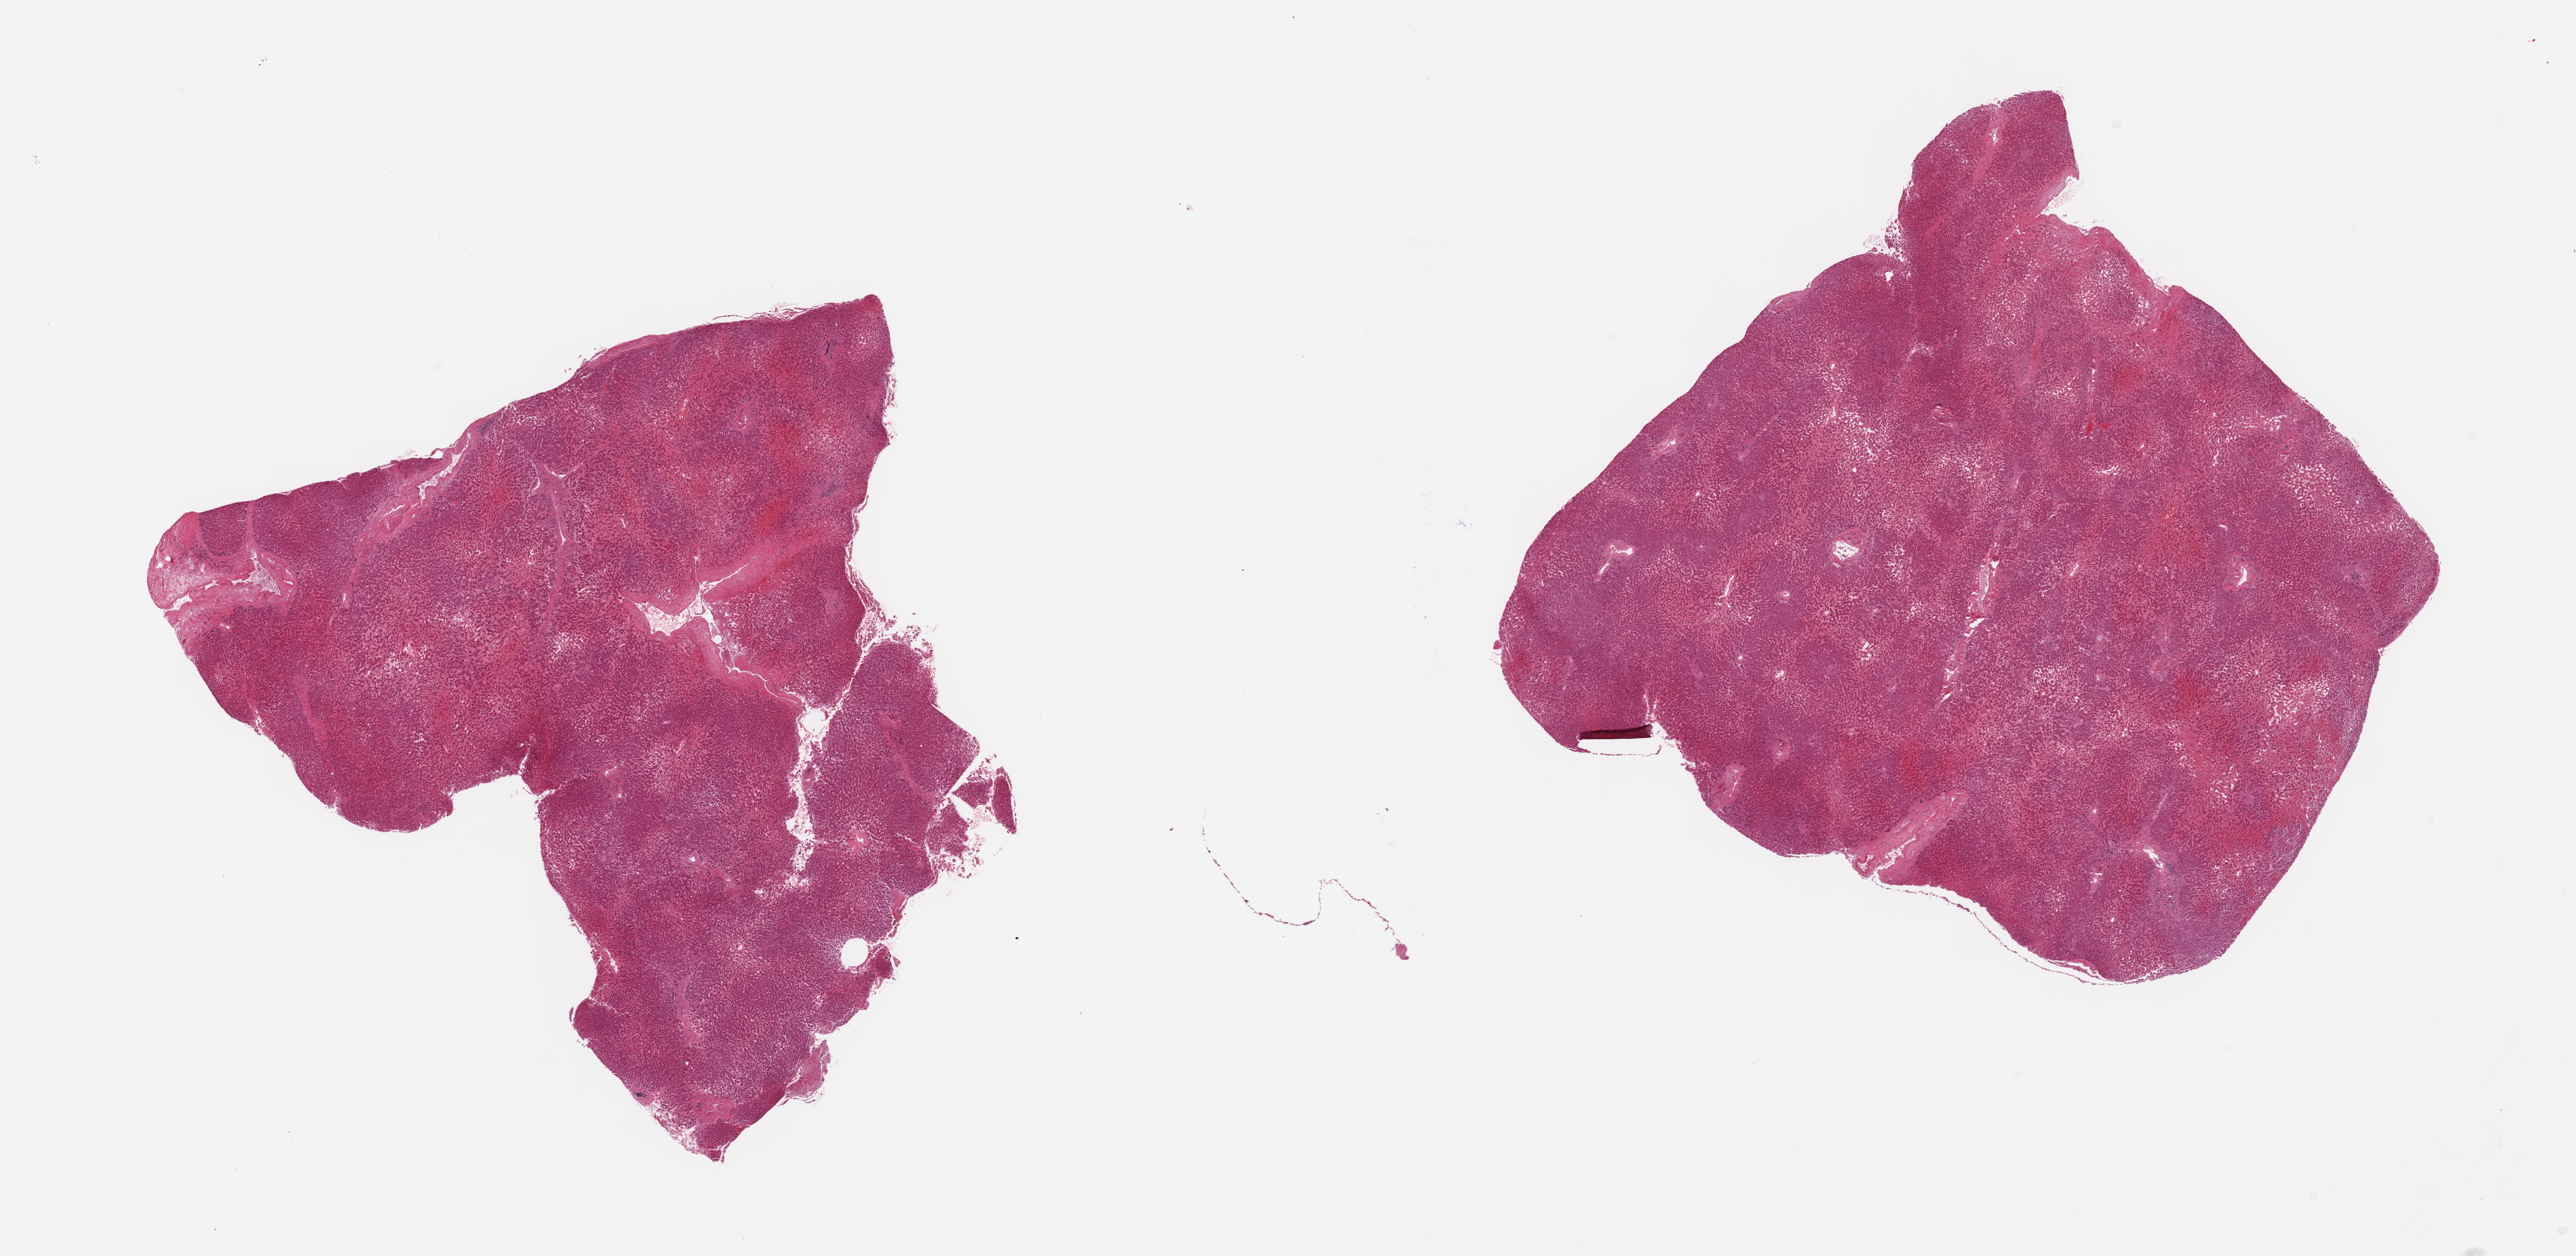
Whole-slide image, hematoxylin and eosin (H&E) stain, low-resolution overview of the scanned area, about 28.5 x 13.9 mm (from a 20x scan), PAXgene-fixed paraffin-embedded (PFPE) section, sampled site (target tissue): liver, tissue donor sample. Donor sex: male.
Review note (as recorded): 2 pieces; moderate centrilobular congestion.